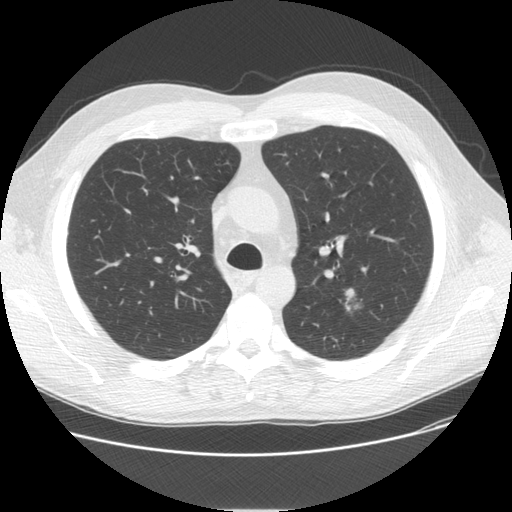
Chest CT (low-dose screening protocol), one axial image; third annual screen; lung window (W 1500 / L -600 HU); 120 kVp; 512 × 512 image matrix, field of view 370 × 370 mm. Male participant, aged 57 years at enrolment. Current smoker at enrolment.
Expert-annotated lung lesion, bounding box [x1, y1, x2, y2] px = [323, 281, 373, 324]. Reader record for this screening exam (exam-level; its link to the box is not recorded): non-calcified nodule or mass ≥4 mm, left upper lobe, 17 × 13 mm, spiculated (stellate) margins, mixed attenuation, pre-existing on the prior screen: yes; interval growth: yes. Official screen result: positive, other. Lung cancer was diagnosed 64 days after this screen: adenosquamous carcinoma, left upper lobe, poorly differentiated (G3), stage IA (AJCC 6th edition), 15 mm at pathology.